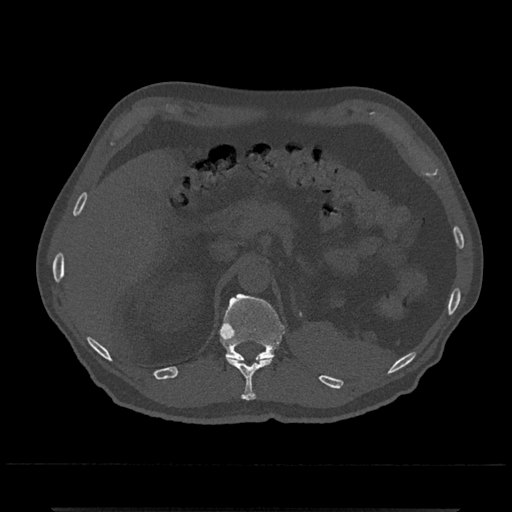
CT including the spine, one axial slice; slice 456 of 797 in the series (ordered by position); bone window (W 1800 / L 400 HU); 0.5 mm slice thickness; 512 × 512 image matrix. Male patient, age 67 years. Case-level facts recorded for this patient, not image findings: primary cancer: prostate.
Annotated regions visible in this slice (semi-automatic segmentation, software-assisted and operator-edited):
- T11 vertebra: box from (x=226, y=356) to (x=274, y=400) px
- T12 vertebra: (x=218, y=294)–(x=285, y=362)